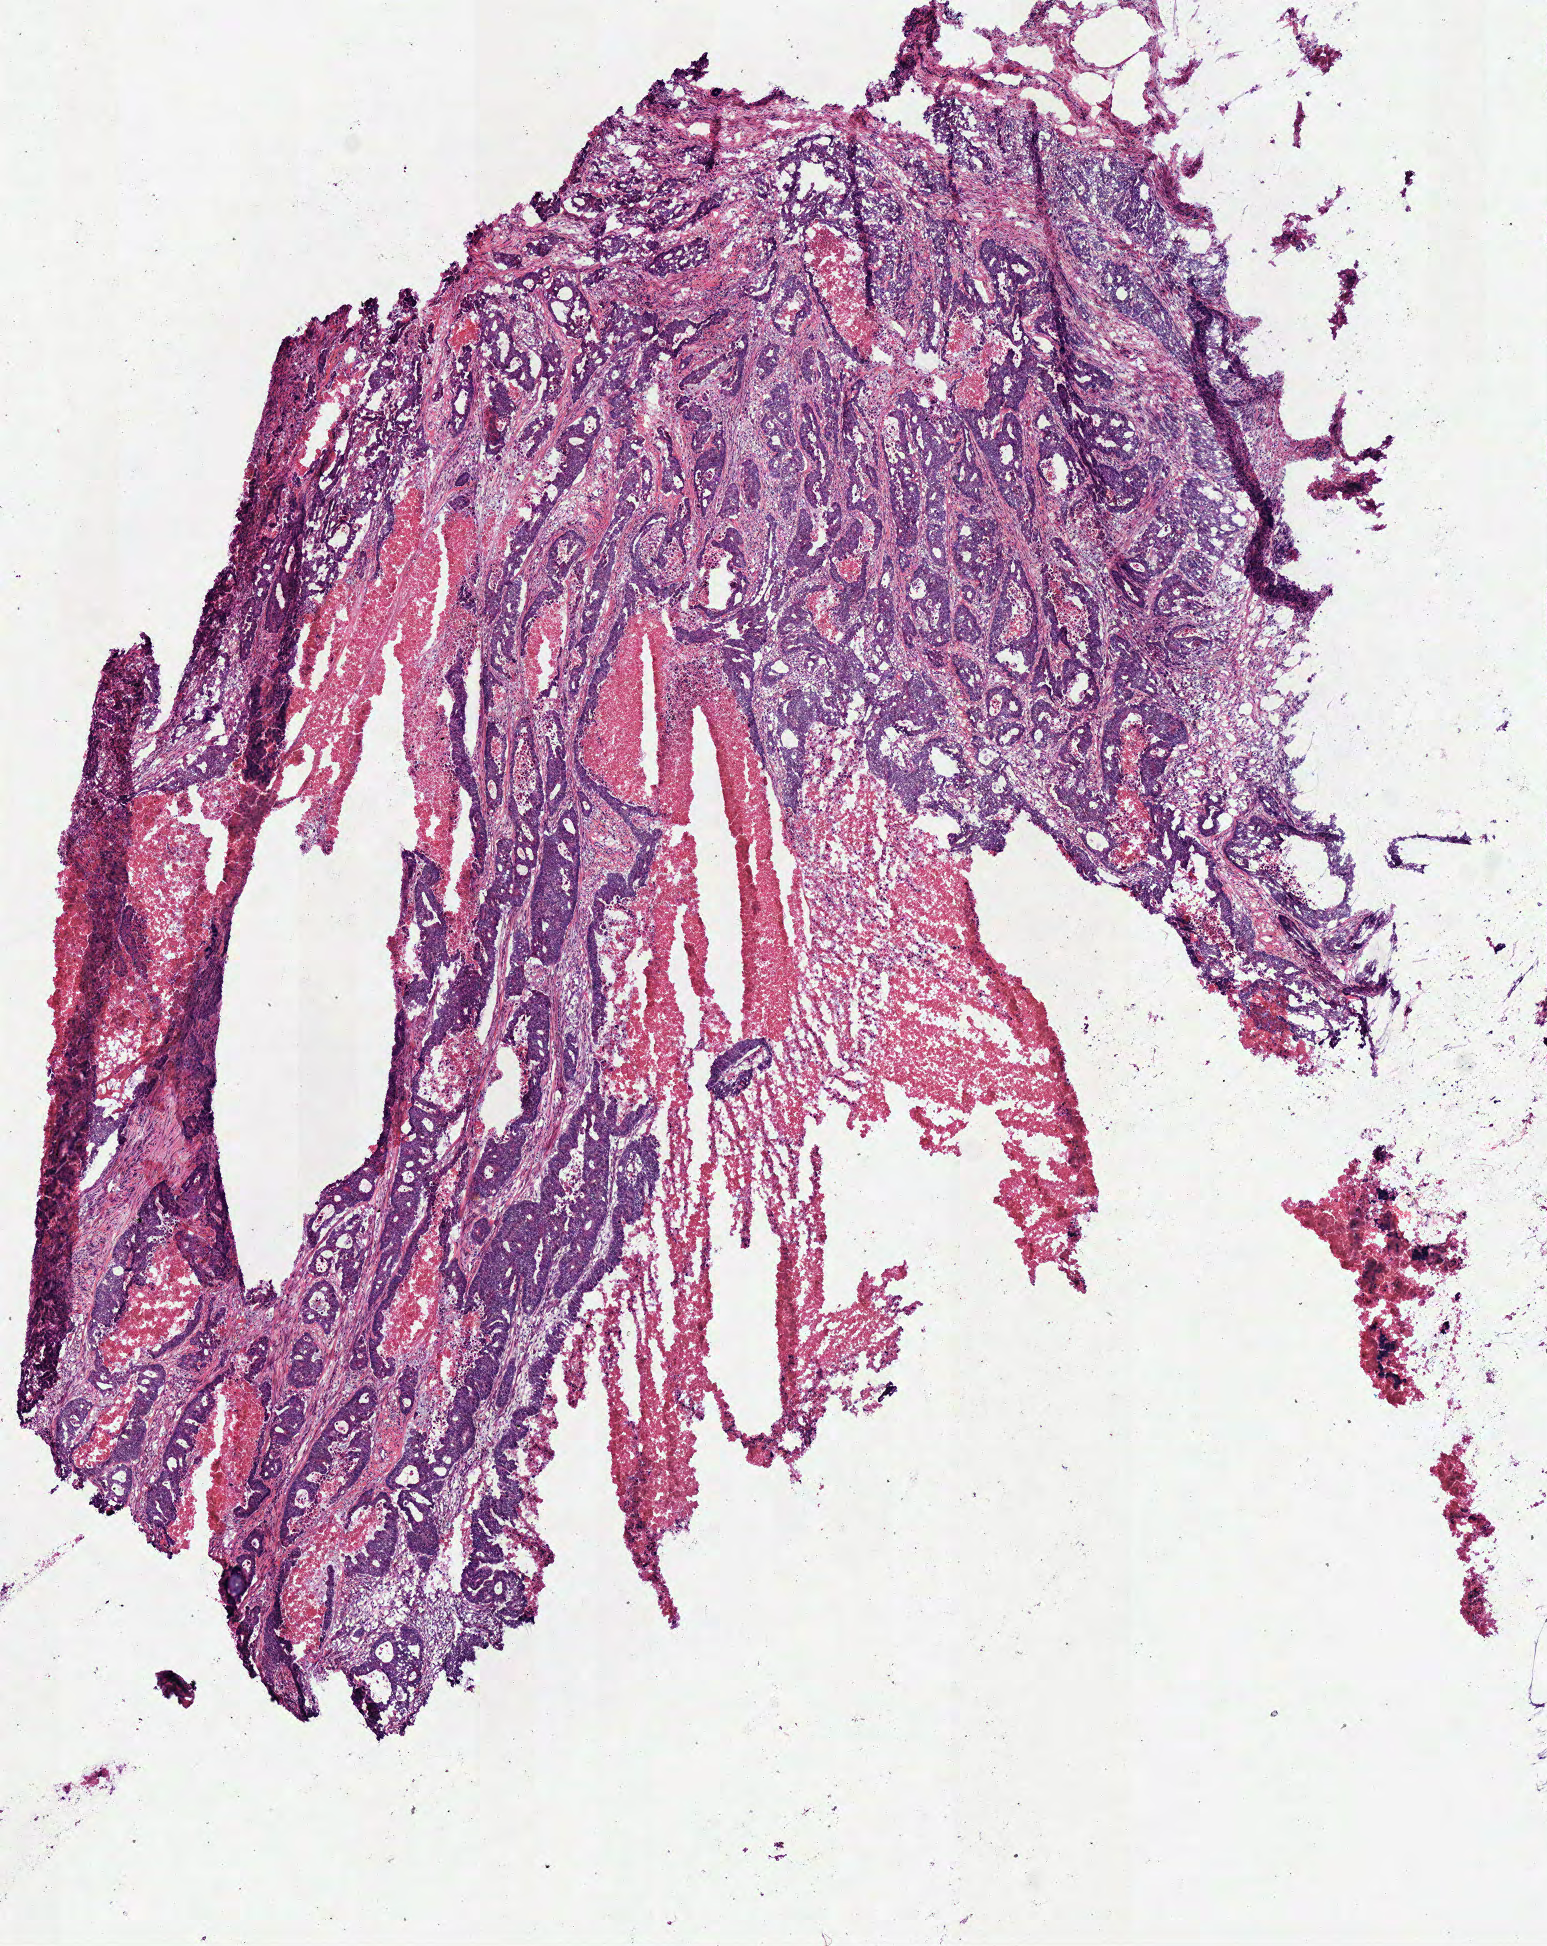
Digitized H&E-stained tissue section (whole slide) — a low-resolution overview of the entire scanned area, about 6.1 x 7.7 mm (from a 40x scan). Frozen section from the bottom of the tissue portion. Primary tumour sample from the colon. Male patient; age at initial diagnosis 69 years. Slide review estimates, as recorded: tumour cells 65%, tumour nuclei 80%, normal cells 0%, stromal cells 30%, necrosis 5%. Infiltration values recorded for this section: lymphocyte infiltration 1%, monocyte infiltration 0%, neutrophil infiltration 2%.
• AJCC pathologic stage: IIA
• lymph nodes positive (case pathology): 0 of 11 examined
• histologic diagnosis: Adenocarcinoma, NOS